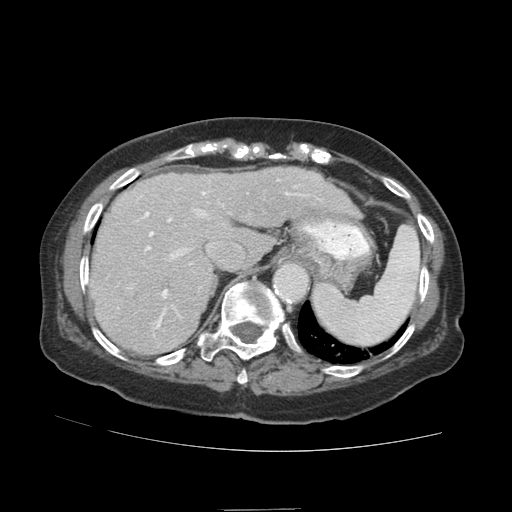
Contrast-enhanced abdominal CT (liver protocol), one axial slice. Slice 68 of 89 in the series (ordered by position). Reconstruction kernel STANDARD. 140 kVp. Soft-tissue window (W 400 / L 40 HU). 512 × 512 image matrix, field of view 360 × 360 mm. Case-level facts recorded for this patient, not image findings: diagnosis: hepatocellular carcinoma (patient treated with transarterial chemoembolisation; whether this scan precedes or follows treatment is not stated here); TNM stage (as recorded): Stage-II; Child-Pugh class: A; tumour differentiation: moderately differentiated; tumour size: 4 cm.
Outlined on this slice (semi-automatic segmentation, software-assisted and operator-edited):
- liver parenchyma outside the tumour (the mass and vessels are separate outlines, so this box may not span the whole liver): bounding box [x1, y1, x2, y2] px = [88, 167, 302, 354]
- liver vessels: [129, 179, 295, 329]